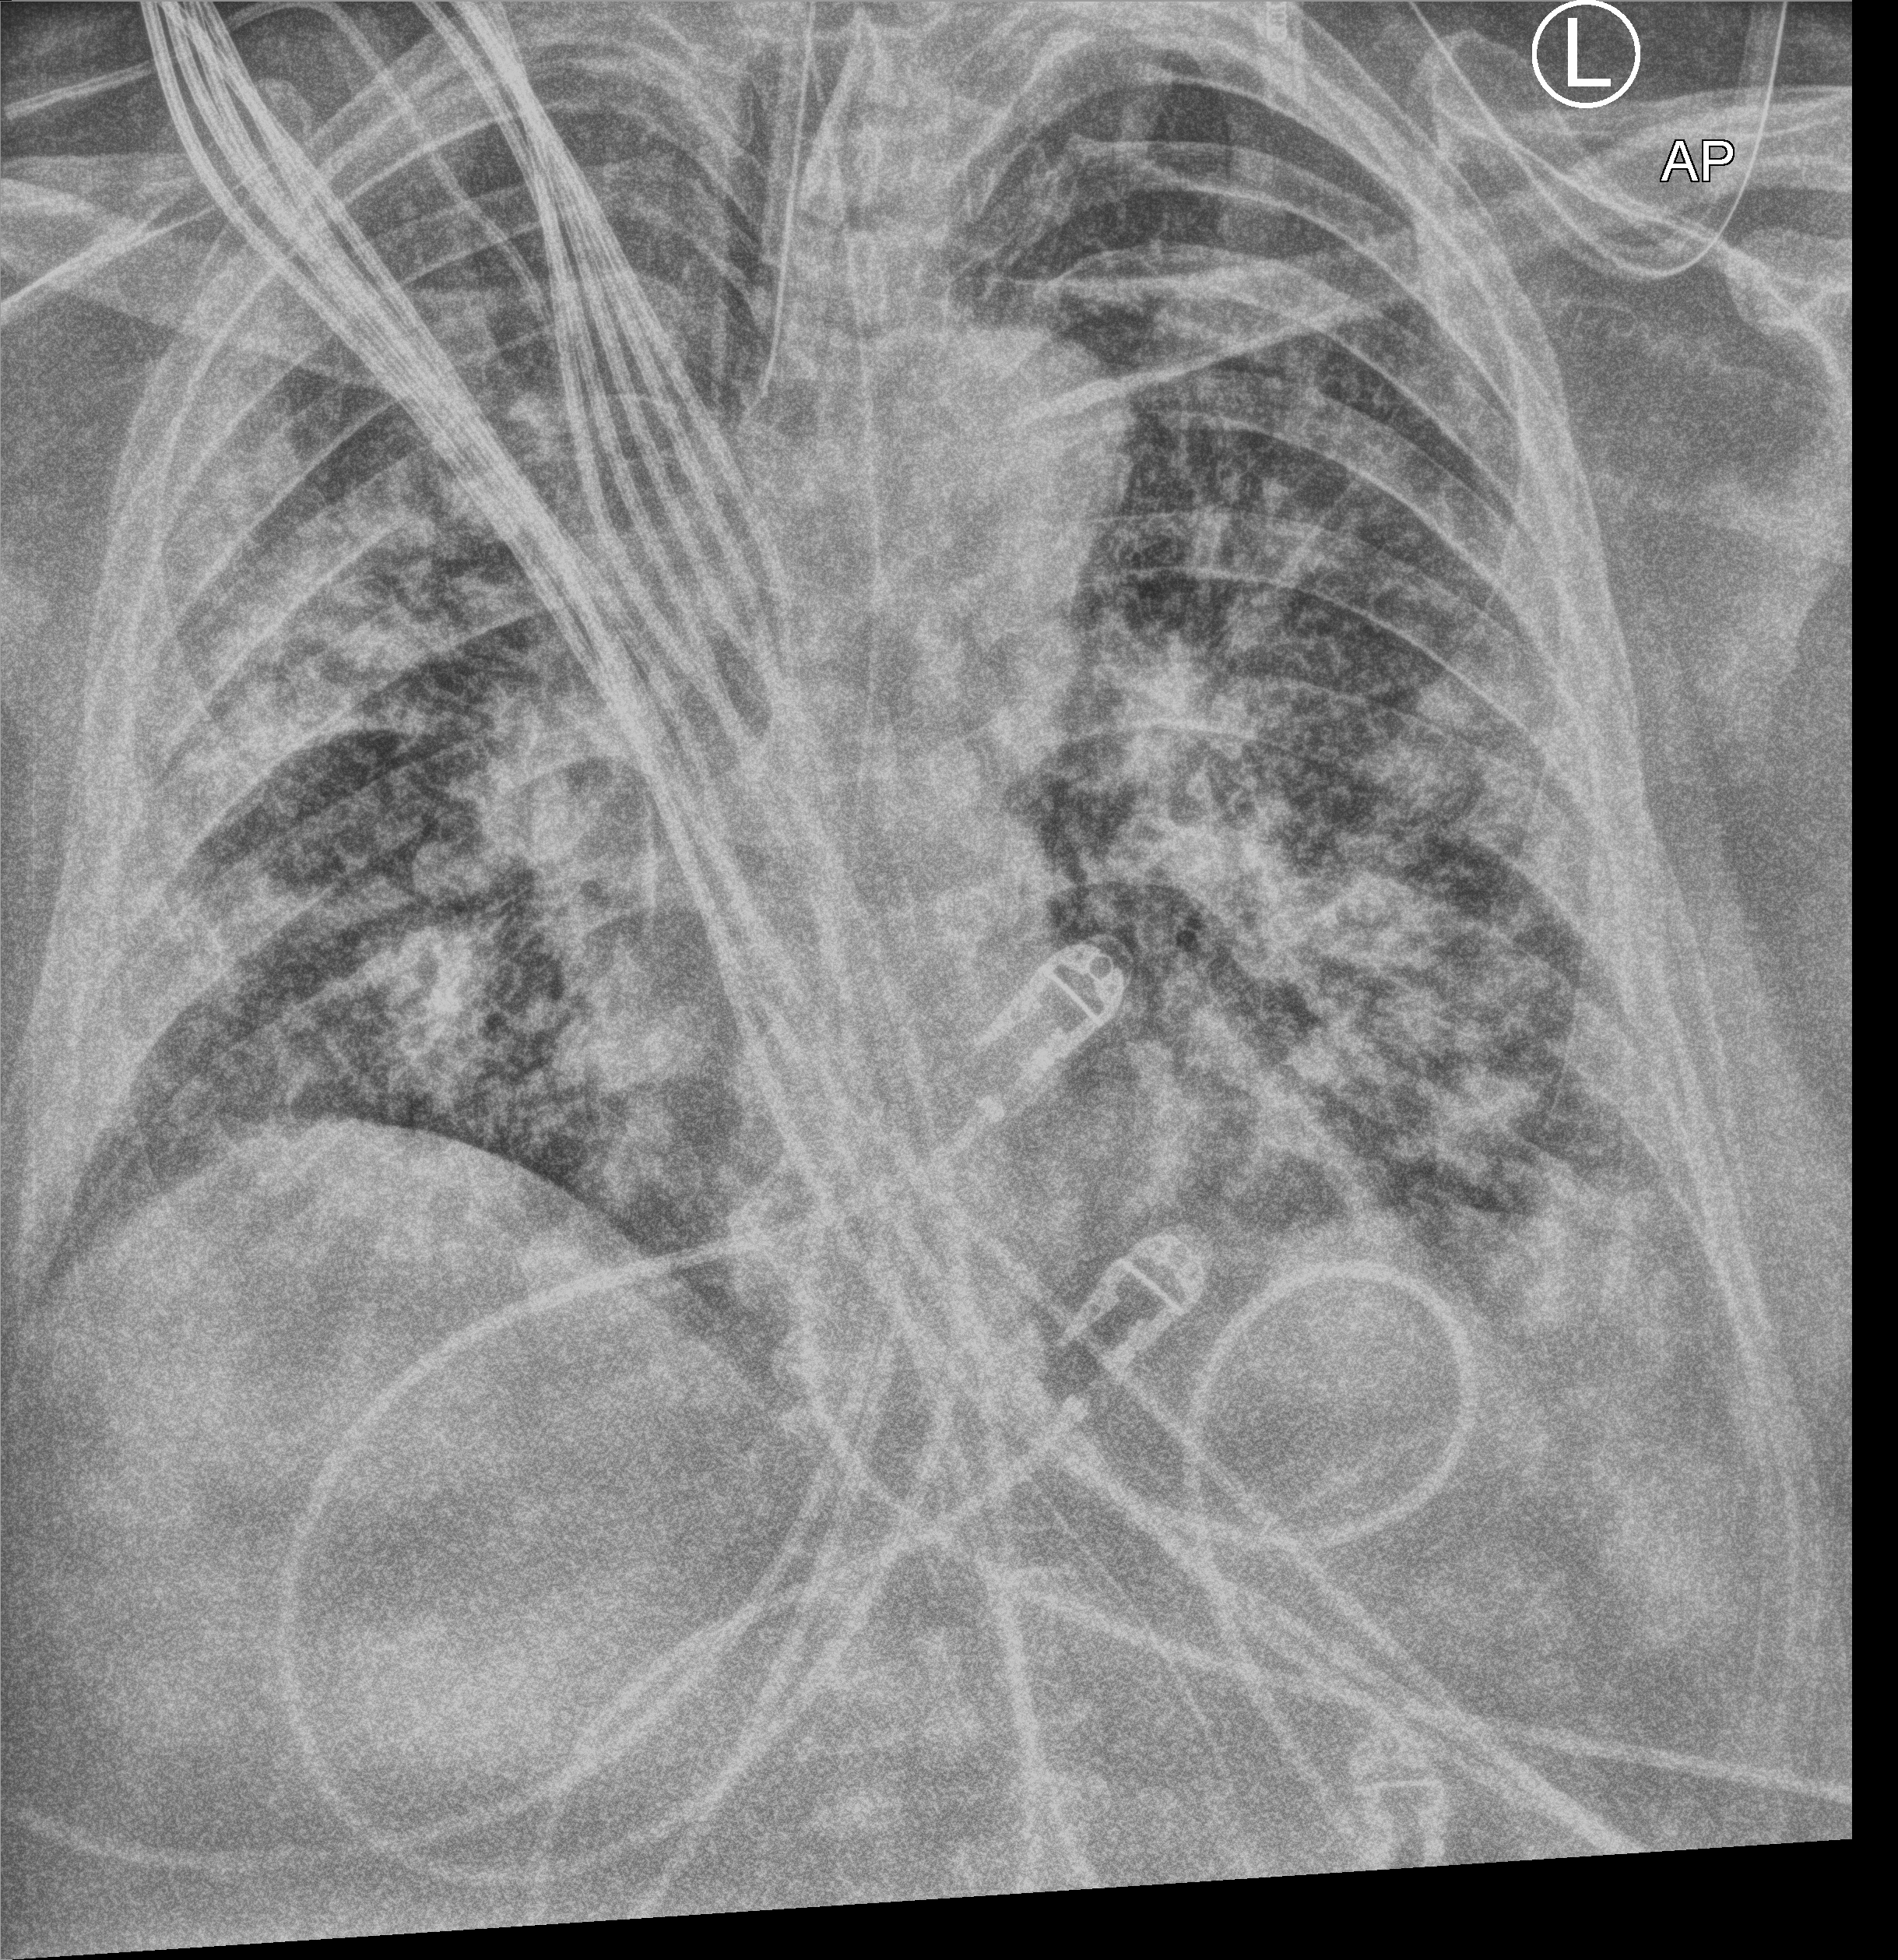
Bedside chest radiograph (computed radiography); anteroposterior (AP) projection. Patient hospitalised with COVID-19, aged 18–59 years.
Hospital-stay facts (about this admission, not read from this image; timing relative to this image not recorded): length of hospital stay: 28 days.